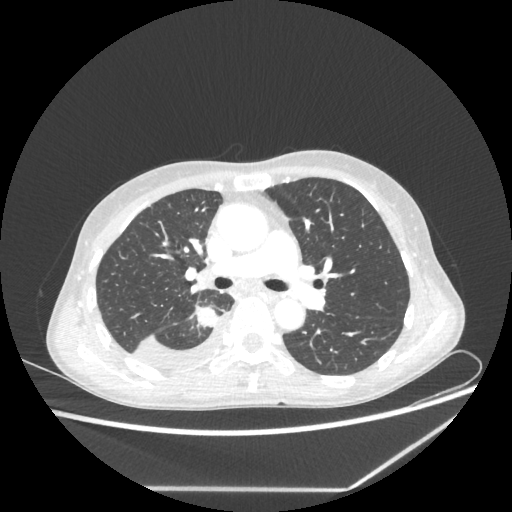
Chest CT, one axial slice. Position 141 of 237 along the scan axis. Lung window (W 1500 / L -600 HU). 512 × 512 image matrix, field of view 364 × 364 mm. Patient: female, 59 years. Case-level facts recorded for this patient, not image findings: clinical TNM (as recorded): T1c N1 M1.
Annotated regions visible in this slice (bounding box drawn by a radiologist):
- lung tumour (recorded histology: adenocarcinoma): bounding box [x1, y1, x2, y2] px = [192, 304, 219, 333]